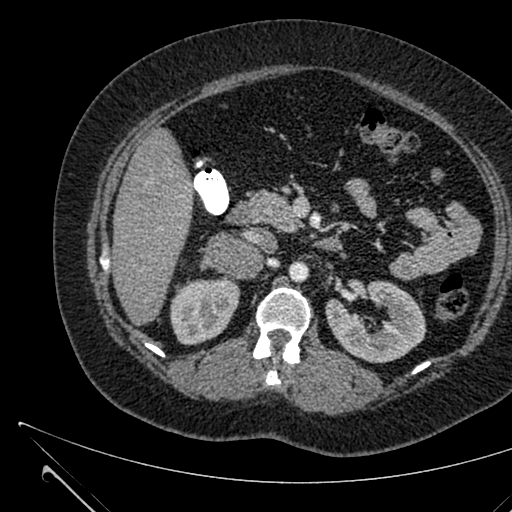
Contrast-enhanced abdominal CT, one axial slice; intravenous contrast given; soft-tissue window (W 400 / L 40 HU); 512 × 512 image matrix, field of view 376 × 376 mm. Patient: female, 36 years. From the clinical record (not read from this slice): diagnosis: adrenocortical carcinoma; tumour side: right adrenal; tumour size at pathology: 10 cm; Ki-67 index: 20 %.
Annotated regions visible in this slice (semi-automatic segmentation, software-assisted and operator-edited):
- mass: box from (x=204, y=234) to (x=258, y=278) px